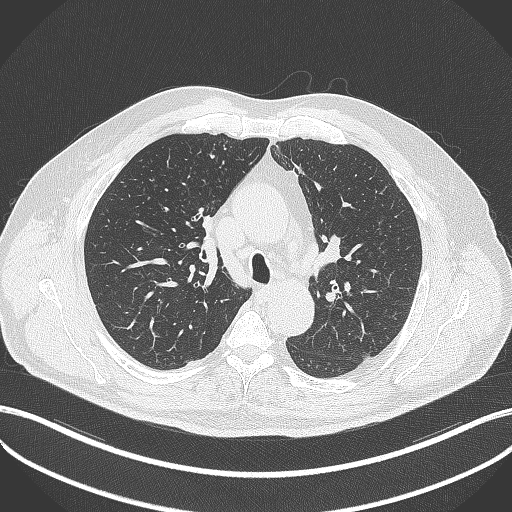
Chest CT, one axial slice. Slice 258 of 411 in the series (ordered by position). 120 kVp. Lung window (W 1500 / L -600 HU). 1 mm slice thickness. 512 × 512 image matrix. Patient: male, 60 years. Case-level facts recorded for this patient, not image findings: clinical TNM (as recorded): T1b N1 M0.
Annotated regions visible in this slice (bounding box drawn by a radiologist):
- lung tumour (recorded histology: squamous cell carcinoma): bounding box <199,214,216,236> (left, top, right, bottom; pixels)